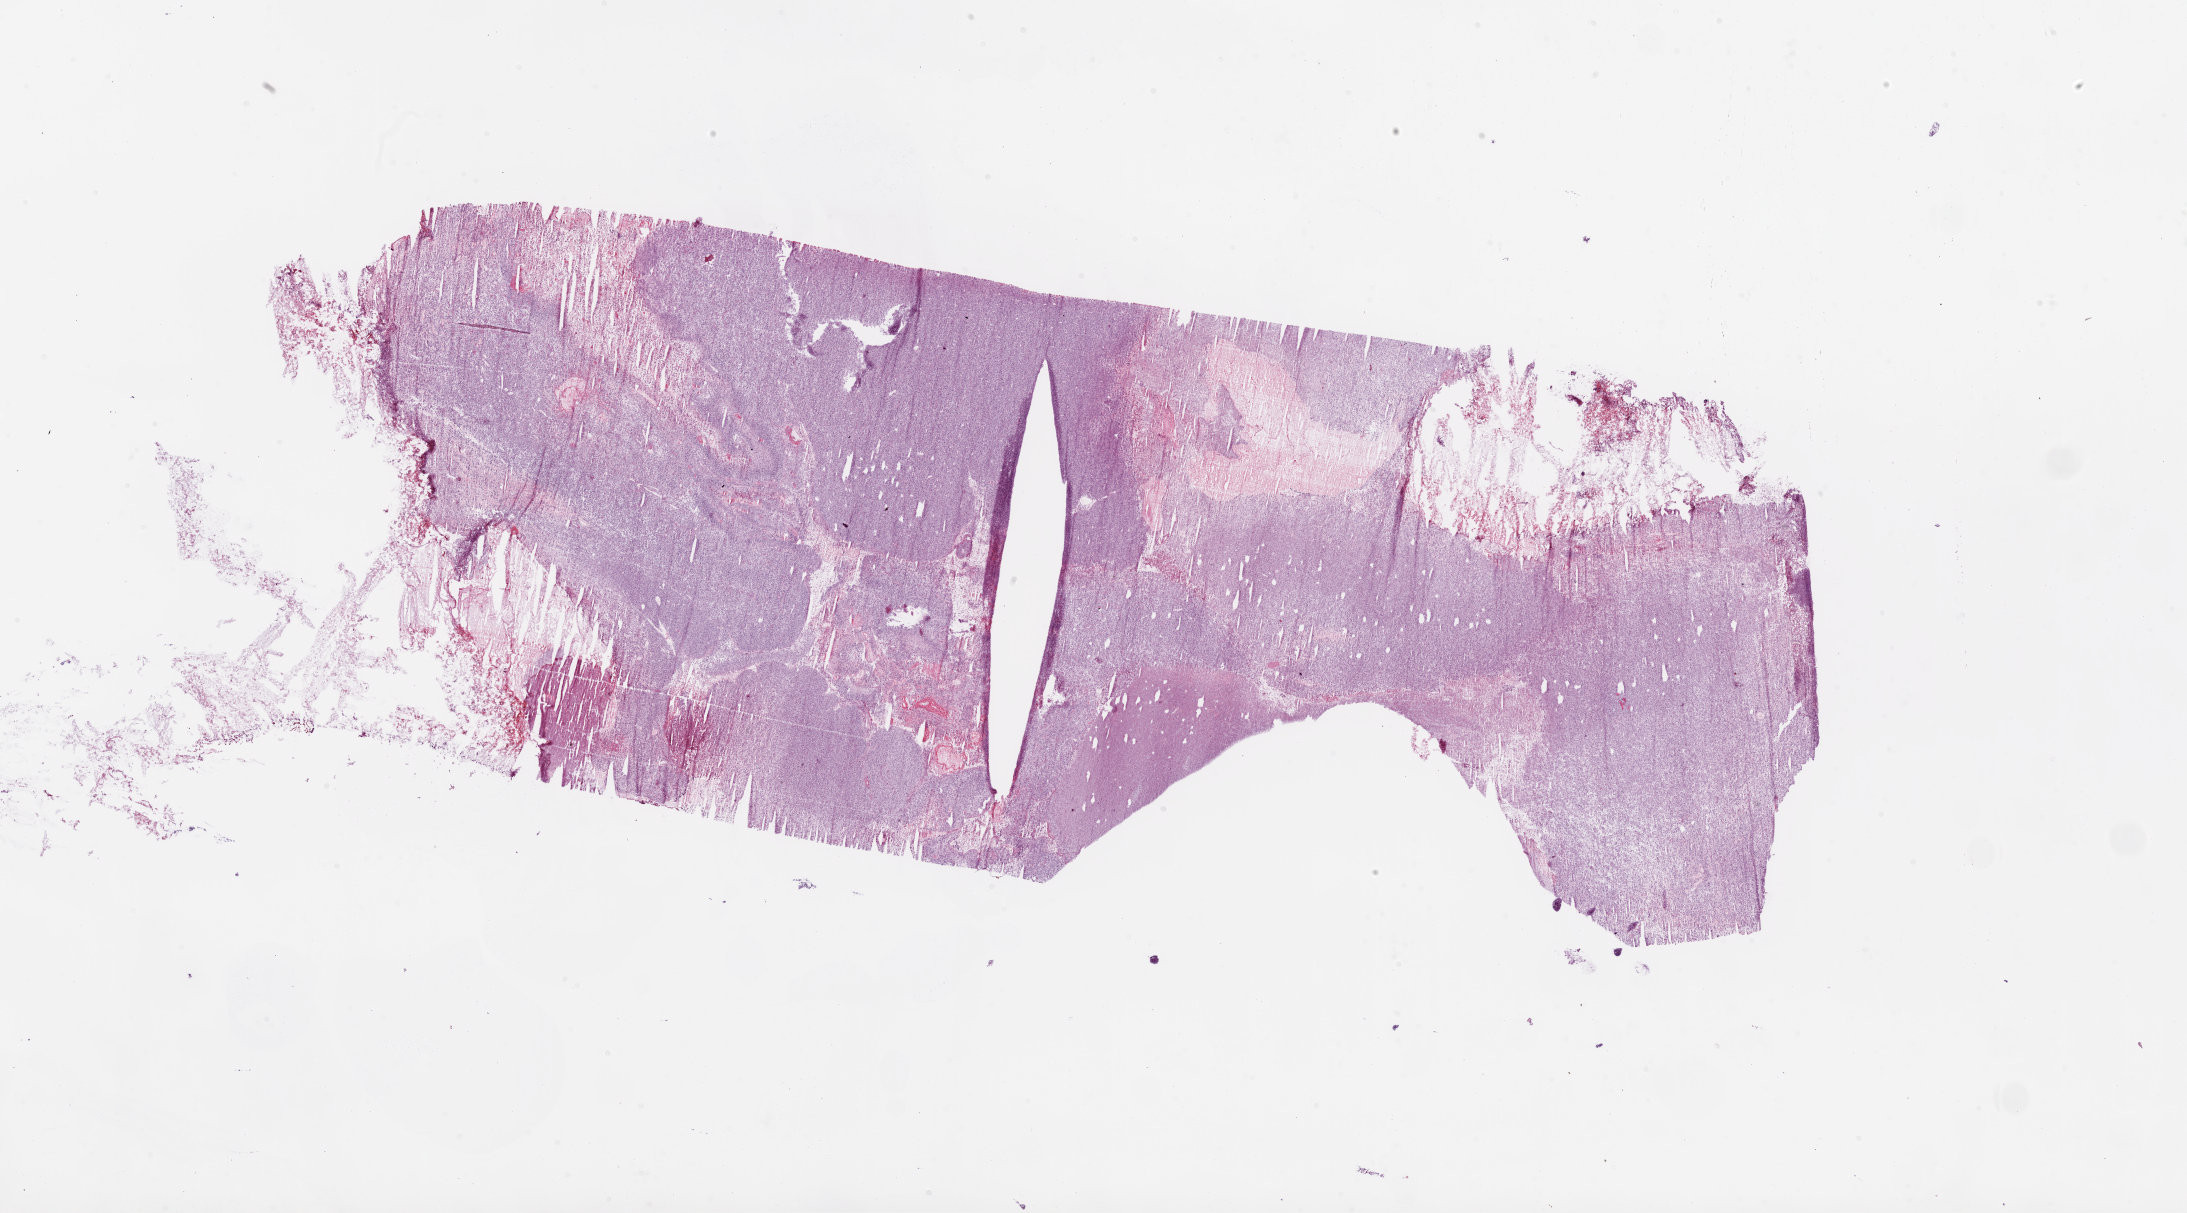
Digitized H&E tissue section (whole slide), a low-resolution overview of the entire scanned area, about 35.1 x 19.5 mm (from a 20x scan), frozen section from the bottom of the tissue portion, primary tumour sample from the brain. Female, age 72 years at initial diagnosis.
Pathologic diagnosis: Glioblastoma.